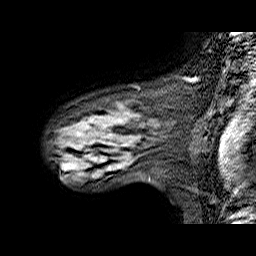
Breast MRI (dynamic contrast-enhanced), one sagittal slice; position 47 of 60 along the scan axis; dynamic contrast-enhanced series, time point 2 of 6 at this slice position (early post-contrast); 1.5 T; TE 6.3 ms, TR 32.9 ms; 256 × 256 image matrix, field of view 200 × 200 mm. Female patient. From the clinical record (not read from this slice): setting: breast cancer imaged before/during neoadjuvant chemotherapy; receptor status: HER2-positive.
Annotated regions visible in this slice (semi-automatic segmentation, software-assisted and operator-edited):
- analysis volume of interest (the breast-tissue region the enhancement analysis was run in; not a lesion): bounding box <55,86,174,173> (left, top, right, bottom; pixels)
- tumour enhancement mask (voxels above the 100 % enhancement threshold inside the analysis volume of interest): <107,167,111,170>